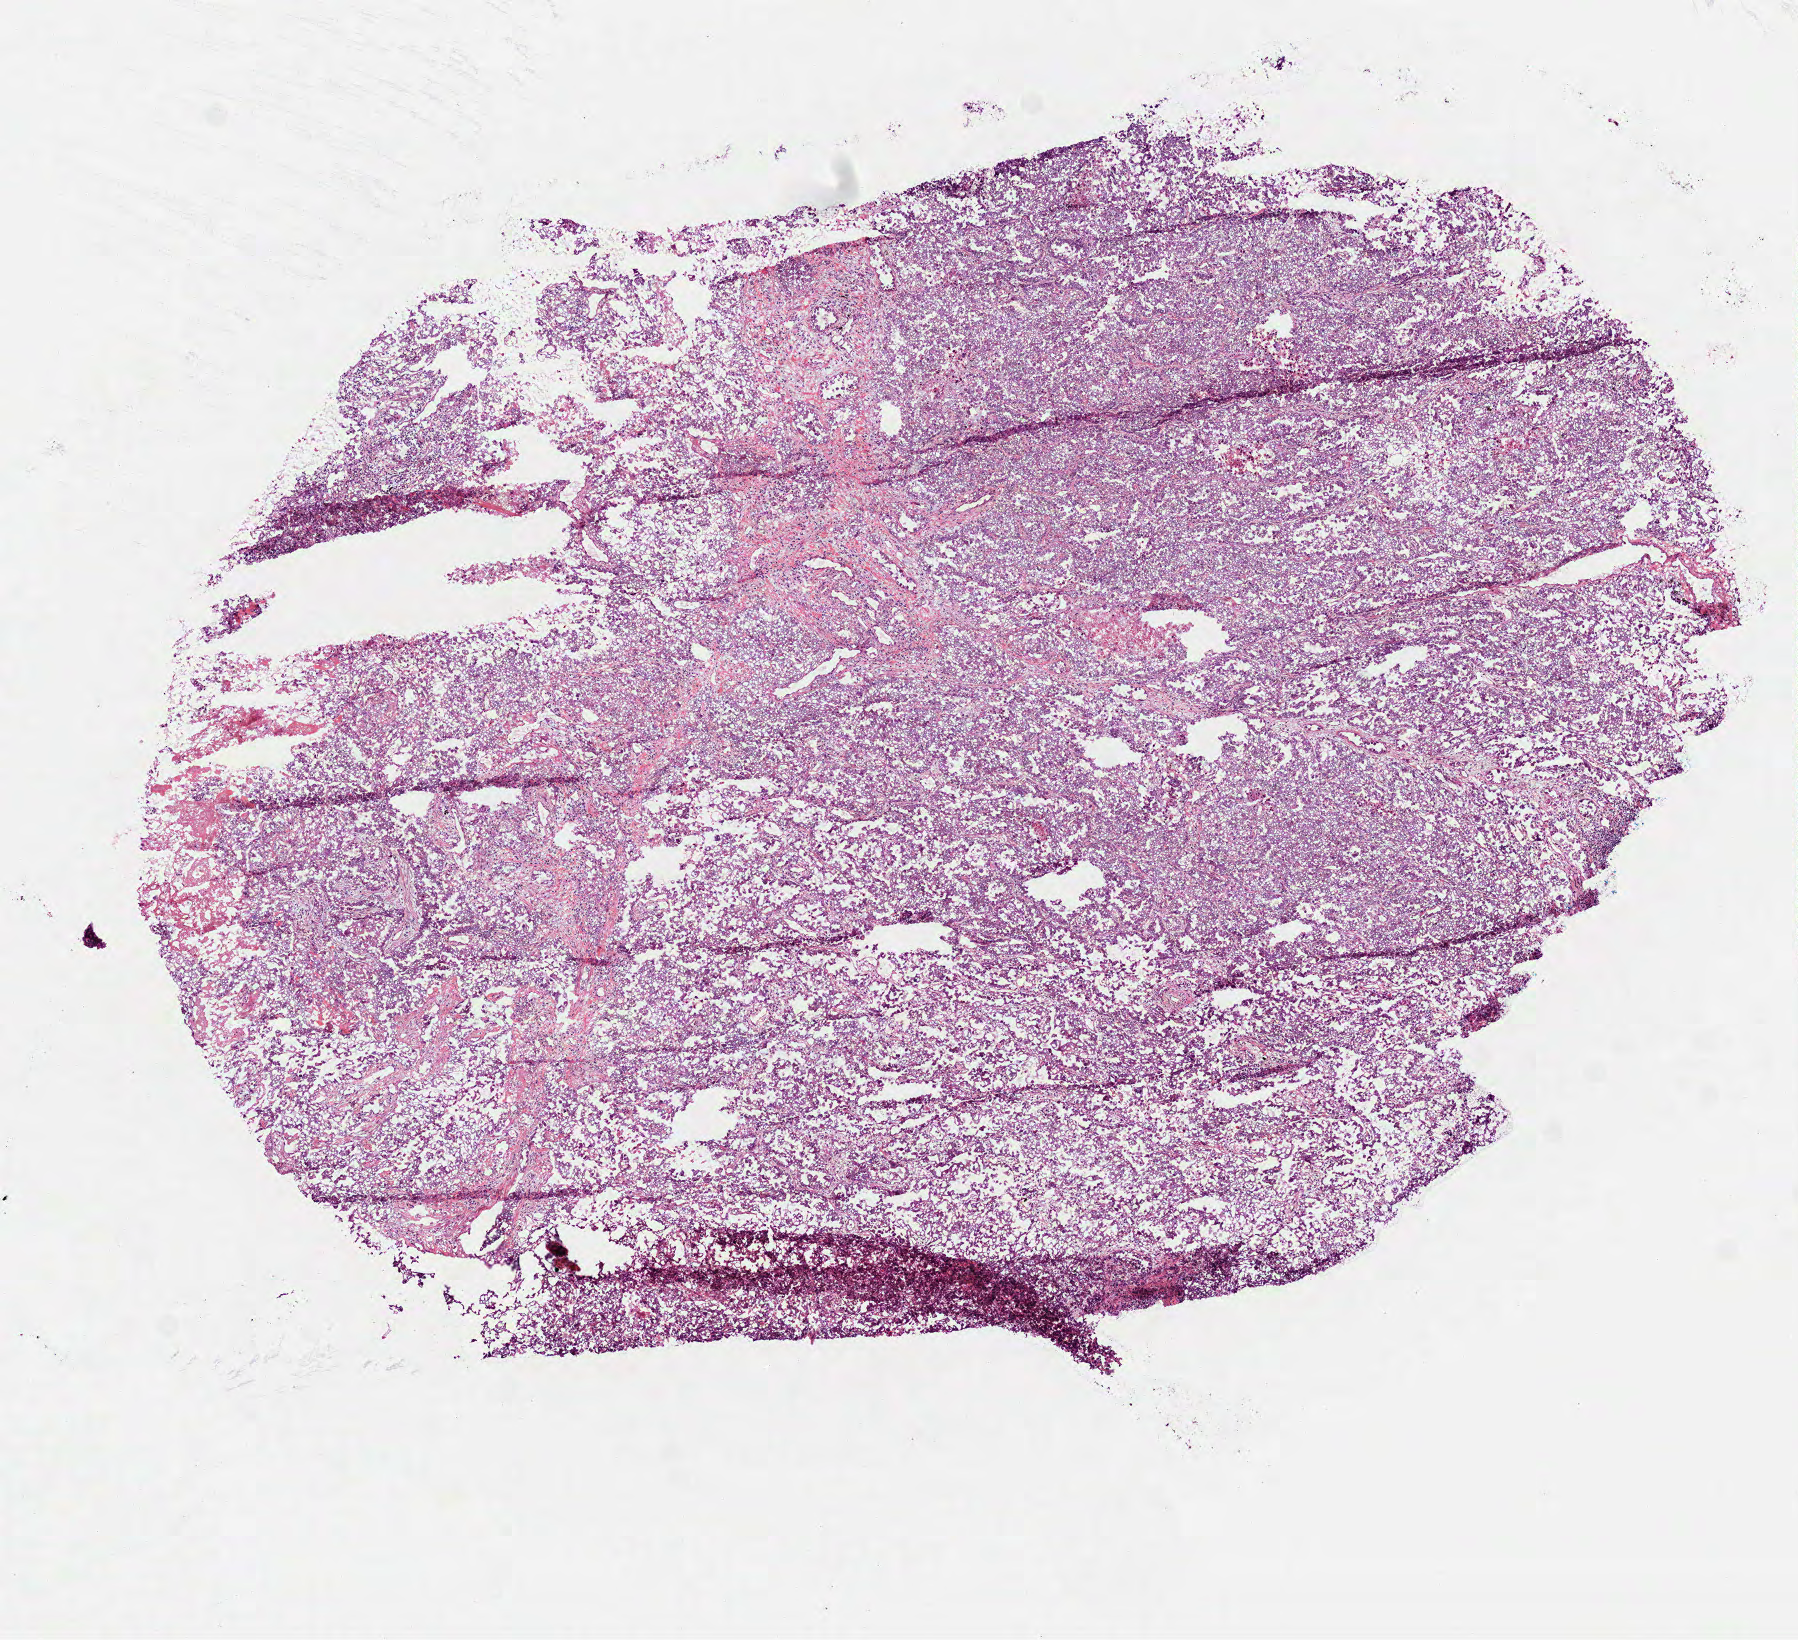
Whole-slide histology image, Hematoxylin and eosin (H&E) stained — low-resolution overview of the scanned area, about 7.3 x 6.6 mm (acquisition: 40x scan); frozen section; sample: primary tumour, lung. Female, age 52 years at initial diagnosis. Pathologist review of this section (percent, as recorded): tumour cells 85%, tumour nuclei 80%, normal cells 0%, stromal cells 10%, necrosis 5%.
- AJCC pathologic stage: IV (6th edition)
- TNM: T4 N1 M1
- laterality: right
- pathologic diagnosis: Adenocarcinoma, NOS (middle lobe, lung)